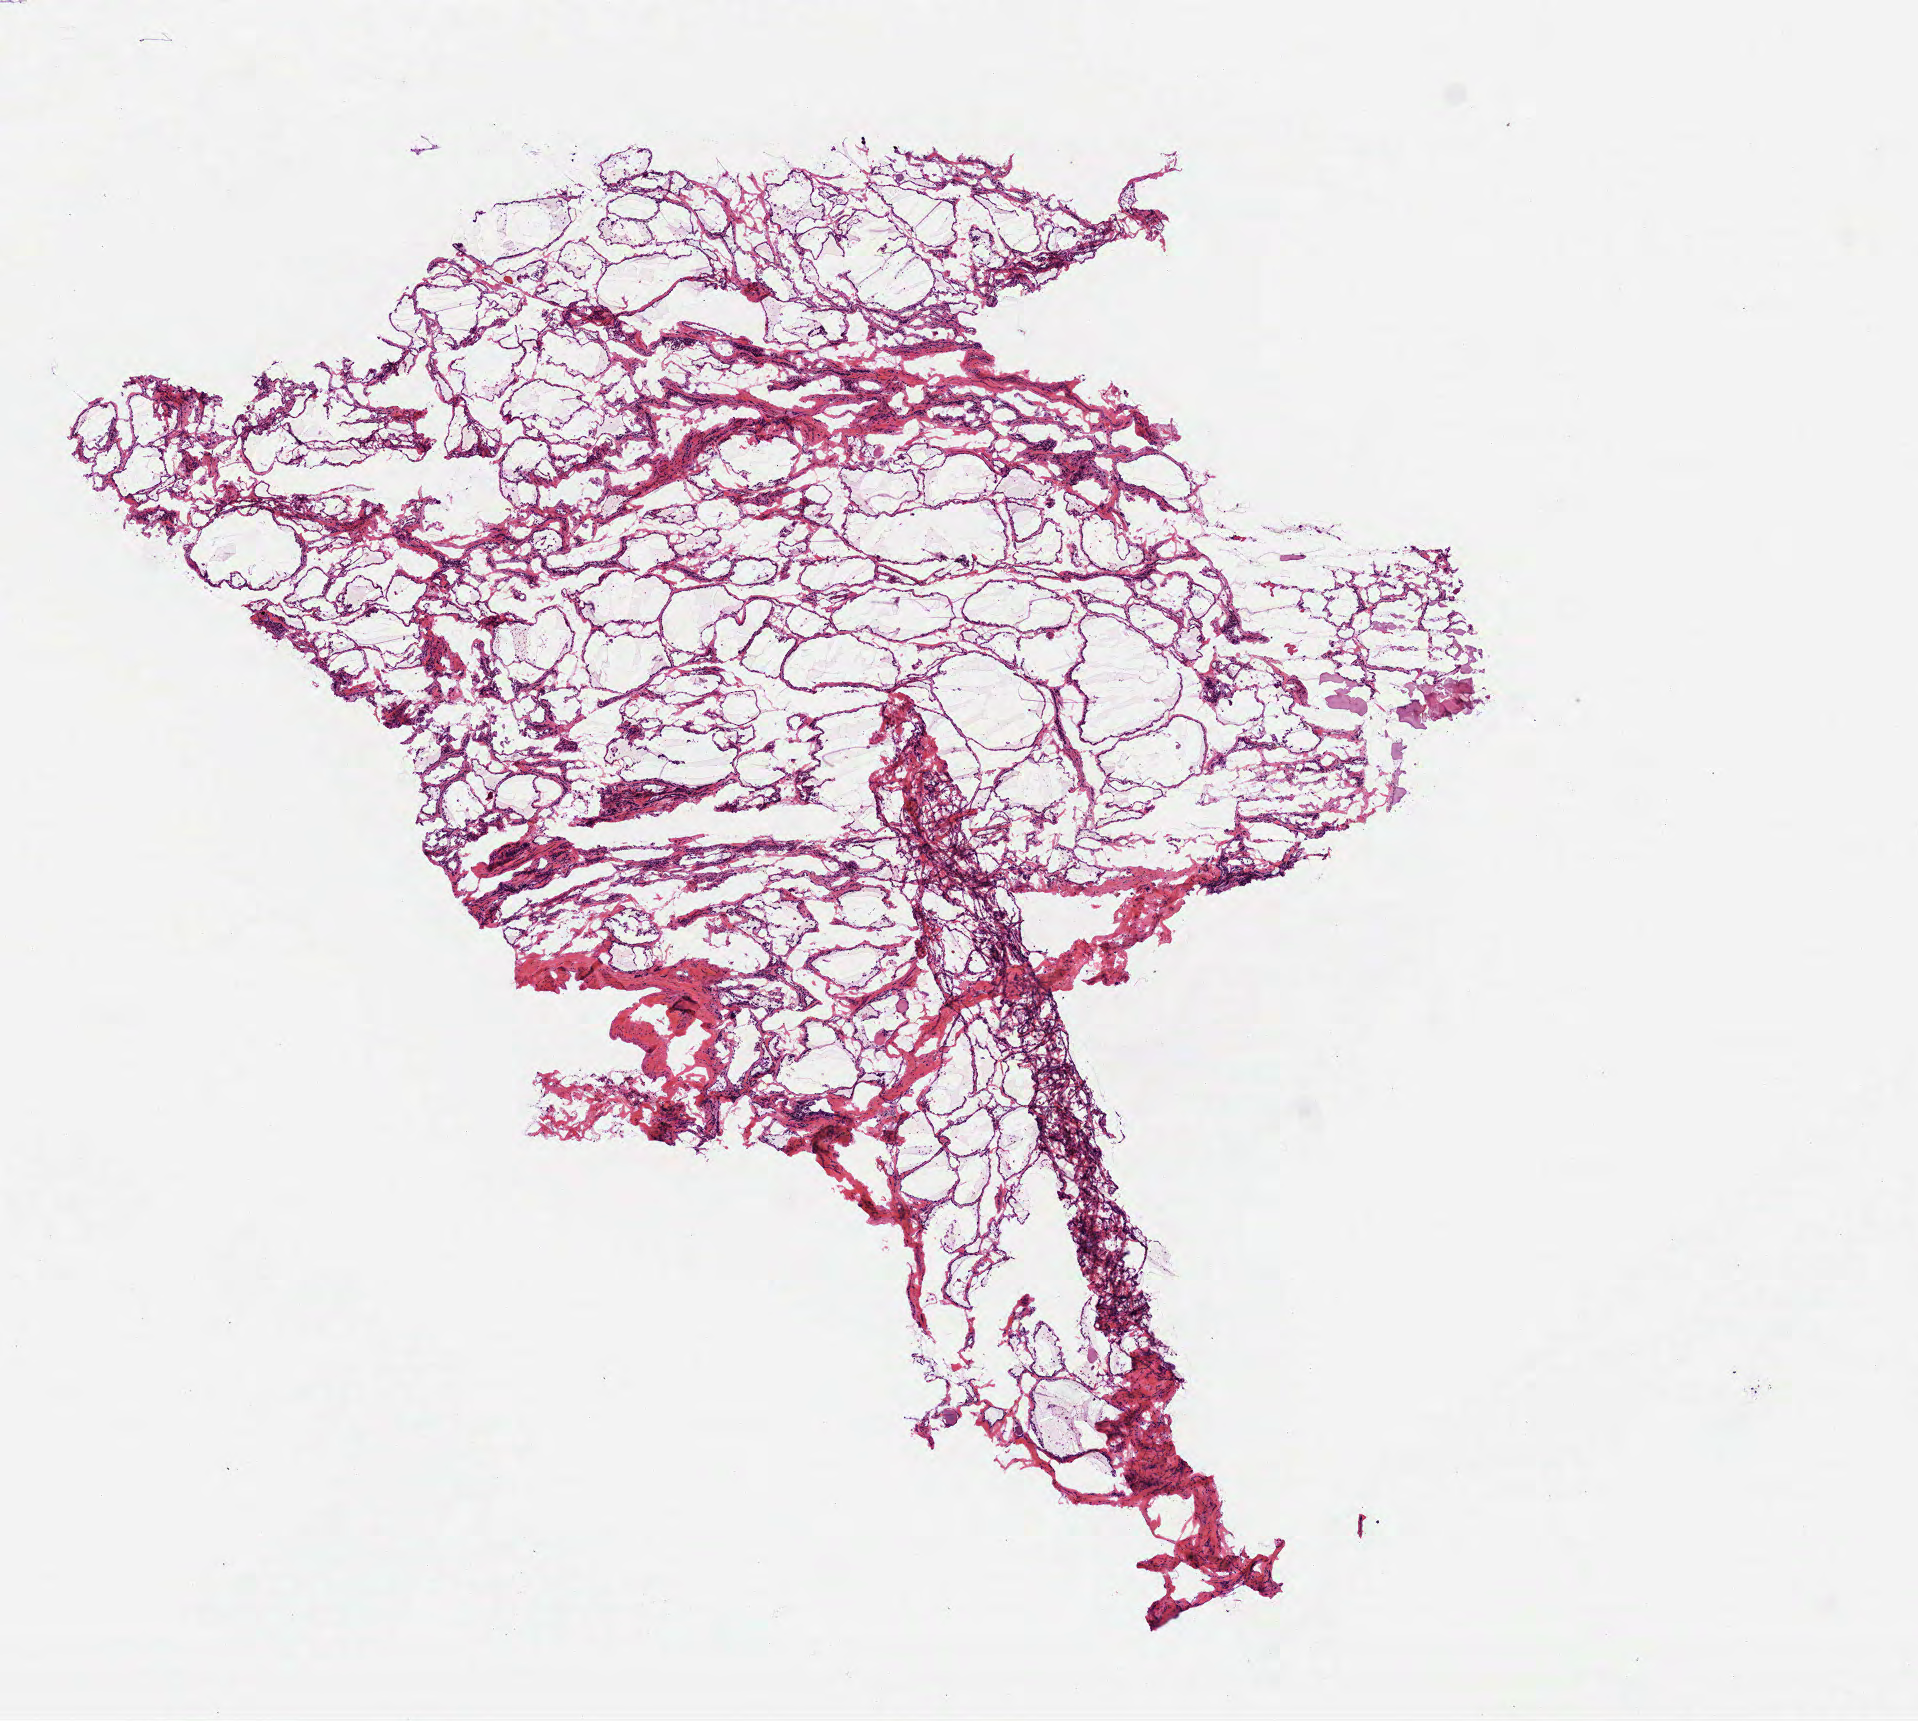
Digitized Hematoxylin and eosin (H&E) stained tissue section (whole slide), low-resolution overview of the scanned area, about 7.7 x 6.9 mm (slide scanned at 40x). Frozen section. Solid tissue normal (non-tumour tissue) sample from the head and neck. Female, age 63 years at initial diagnosis.
• this section: solid tissue normal sample (biorepository sample class)
• patient diagnosis: Squamous cell carcinoma, NOS (larynx, NOS)